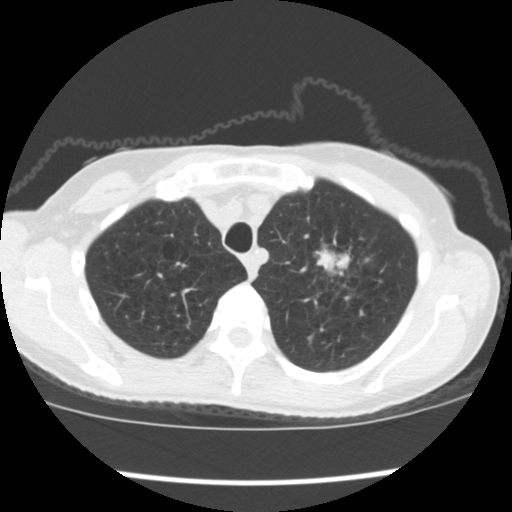
Low-dose screening chest CT, one axial slice; slice 150 of 176 in the series (ordered by position); reconstruction kernel STANDARD; lung window (W 1500 / L -600 HU); 2.5 mm slice thickness; 512 × 512 image matrix, field of view 318 × 318 mm.
Annotated regions visible in this slice (manually delineated by an expert):
- lesion 1 (tumor, upper lobe of left lung): bounding box <317,249,350,277> (left, top, right, bottom; pixels)